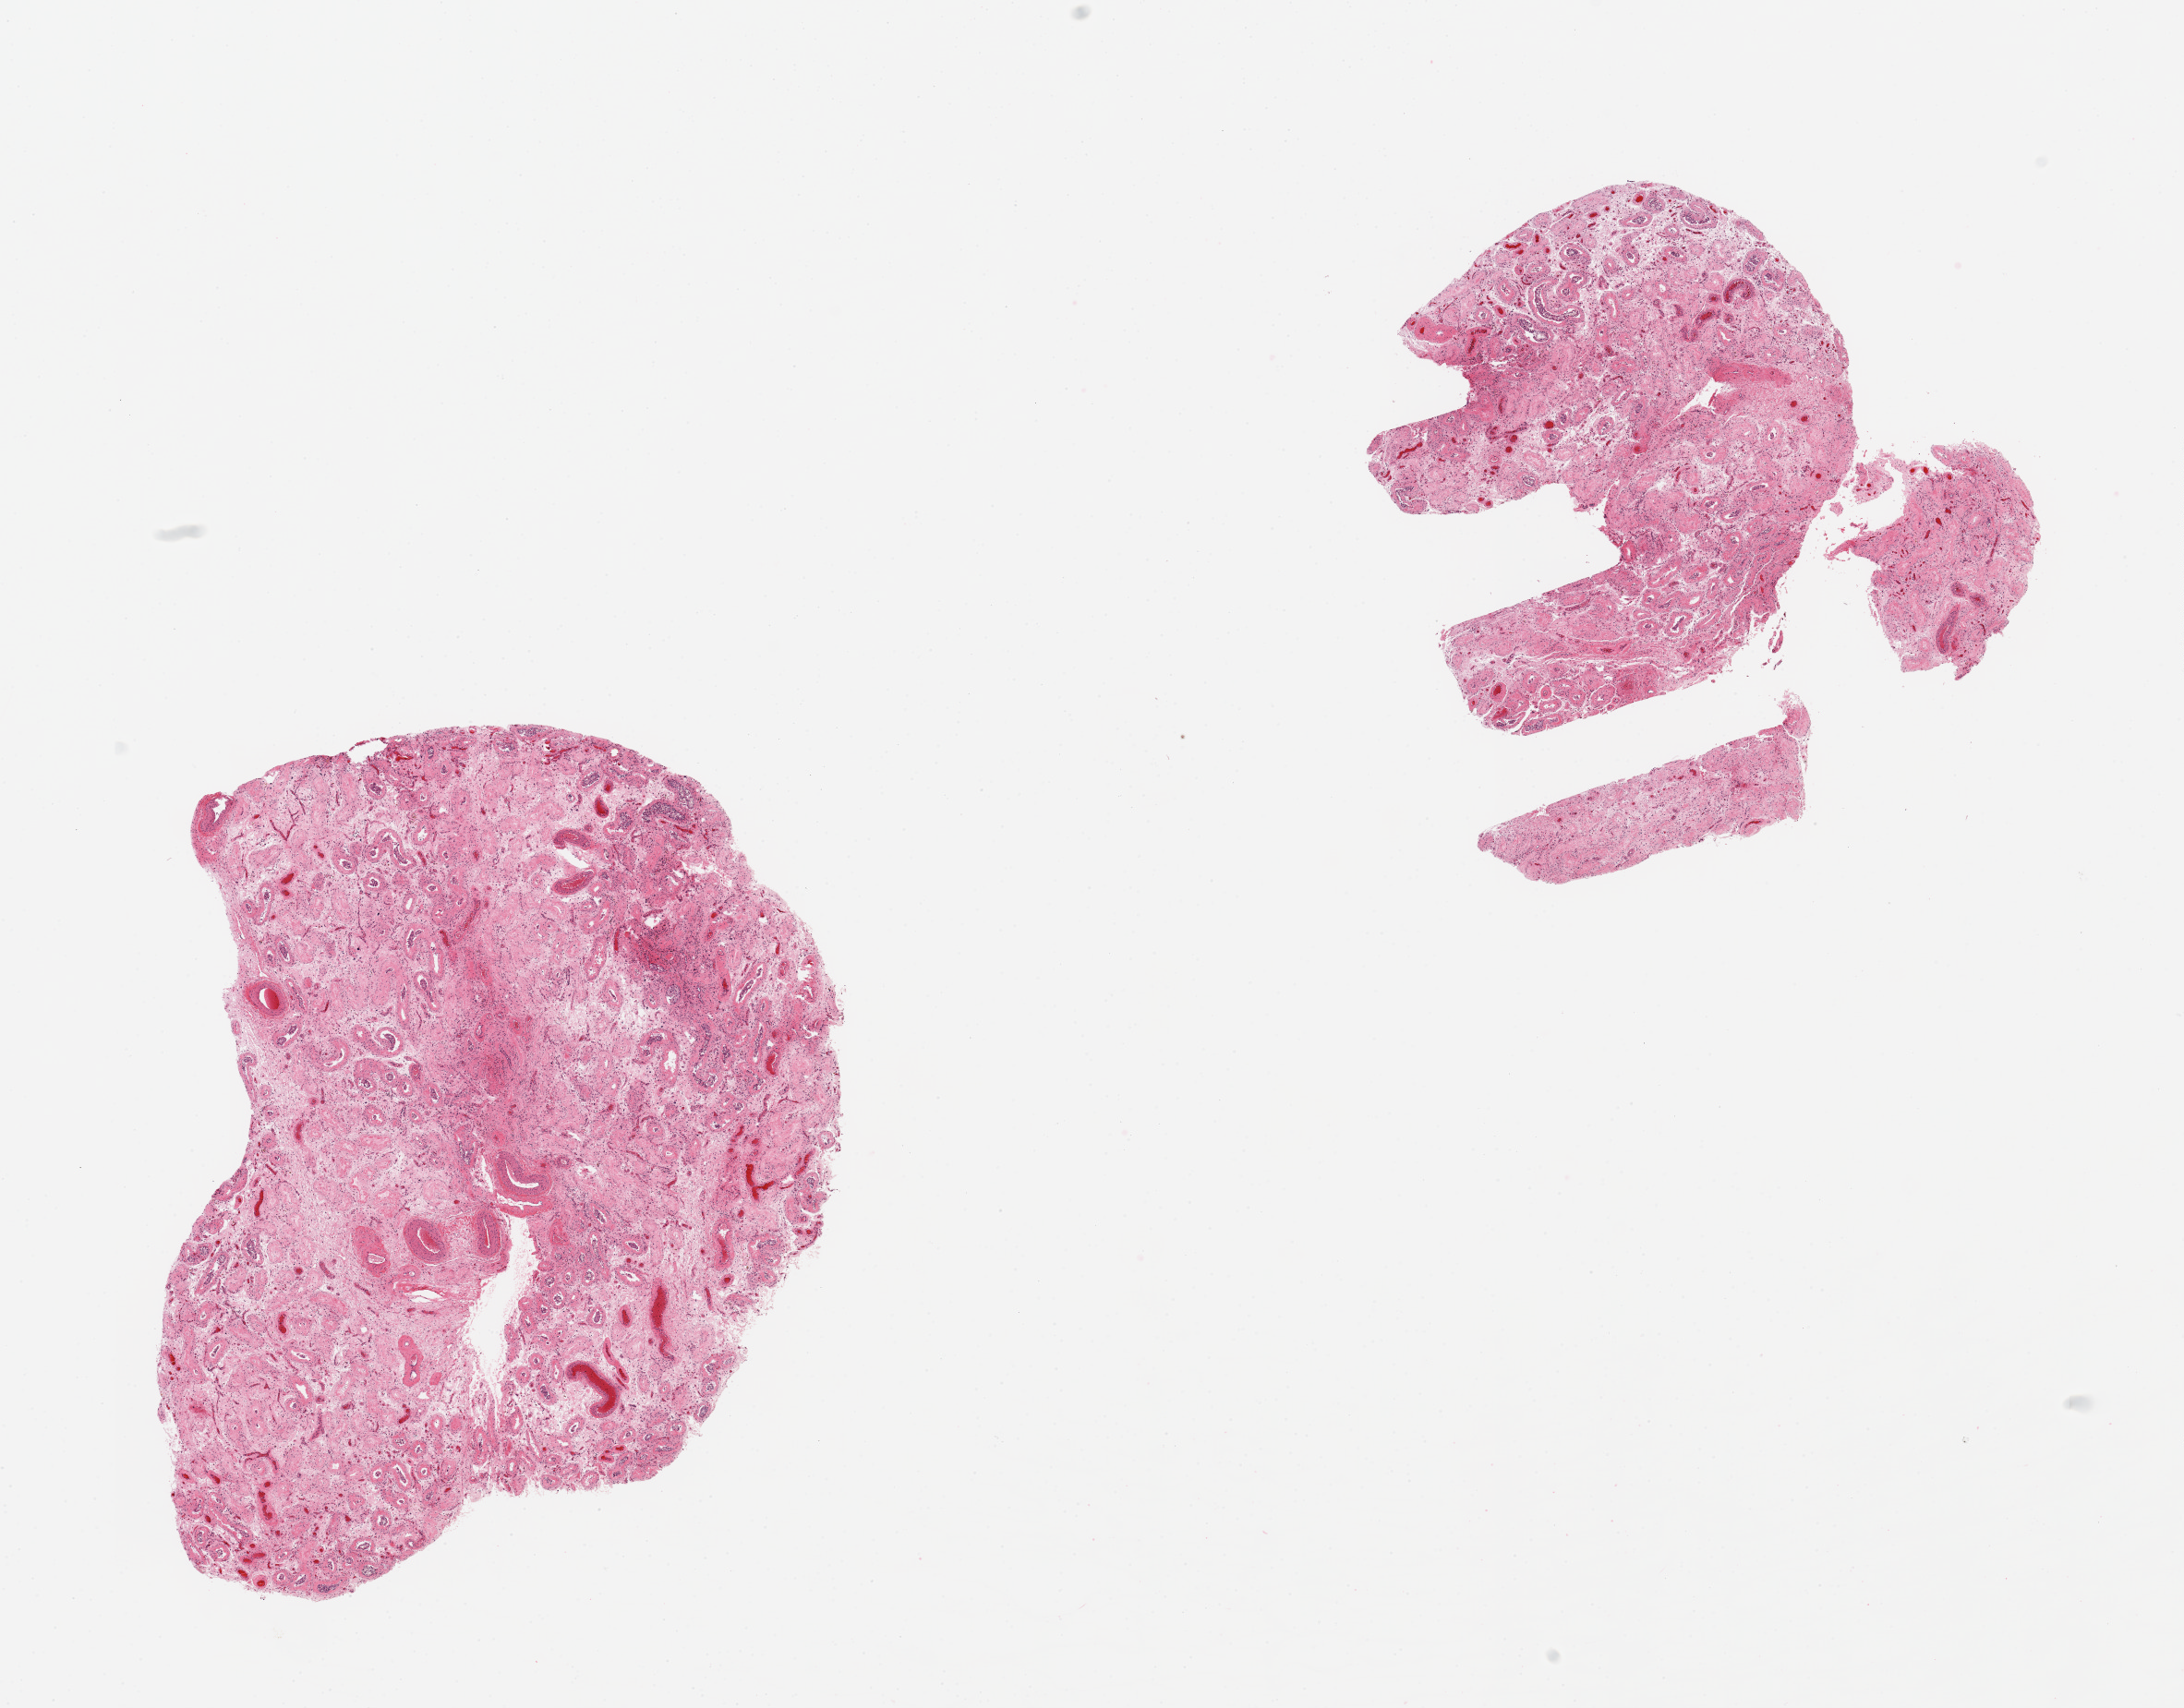
Digitized H&E-stained section, brightfield — shown as a low-resolution overview of the whole scanned area (about 18.7 x 14.6 mm). PAXgene-fixed, paraffin-embedded tissue. Section of testis (target tissue). Tissue donor sample.
Review note (as recorded): 2 pieces, near-total sclerosis/ atrophy of seminiferous tubules, no significant Leydig cell hyperlasia, findings c/w history of cirrhosis.